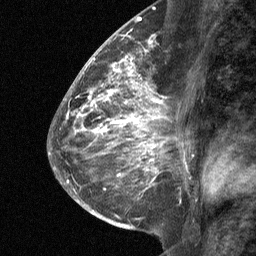
Breast MRI (dynamic contrast-enhanced), one sagittal slice; slice 34 of 64 in the series (ordered by position); dynamic contrast-enhanced study with each time point stored as its own series, time point 2 of 3 at this slice position (early post-contrast, ordered by acquisition time); 1.5 T; TE 4.8 ms, TR 27 ms; 2 mm slice thickness; 256 × 256 image matrix. Female patient, age 59 years. Case-level facts recorded for this patient, not image findings: setting: breast cancer imaged before/during neoadjuvant chemotherapy; receptor status: triple-negative.
Structures marked on this image (semi-automatic segmentation, software-assisted and operator-edited):
- analysis volume of interest (the breast-tissue region the enhancement analysis was run in; not a lesion): bounding box [x1, y1, x2, y2] px = [122, 58, 176, 109]
- tumour enhancement mask (voxels above the 90 % enhancement threshold inside the analysis volume of interest): [122, 58, 165, 109]